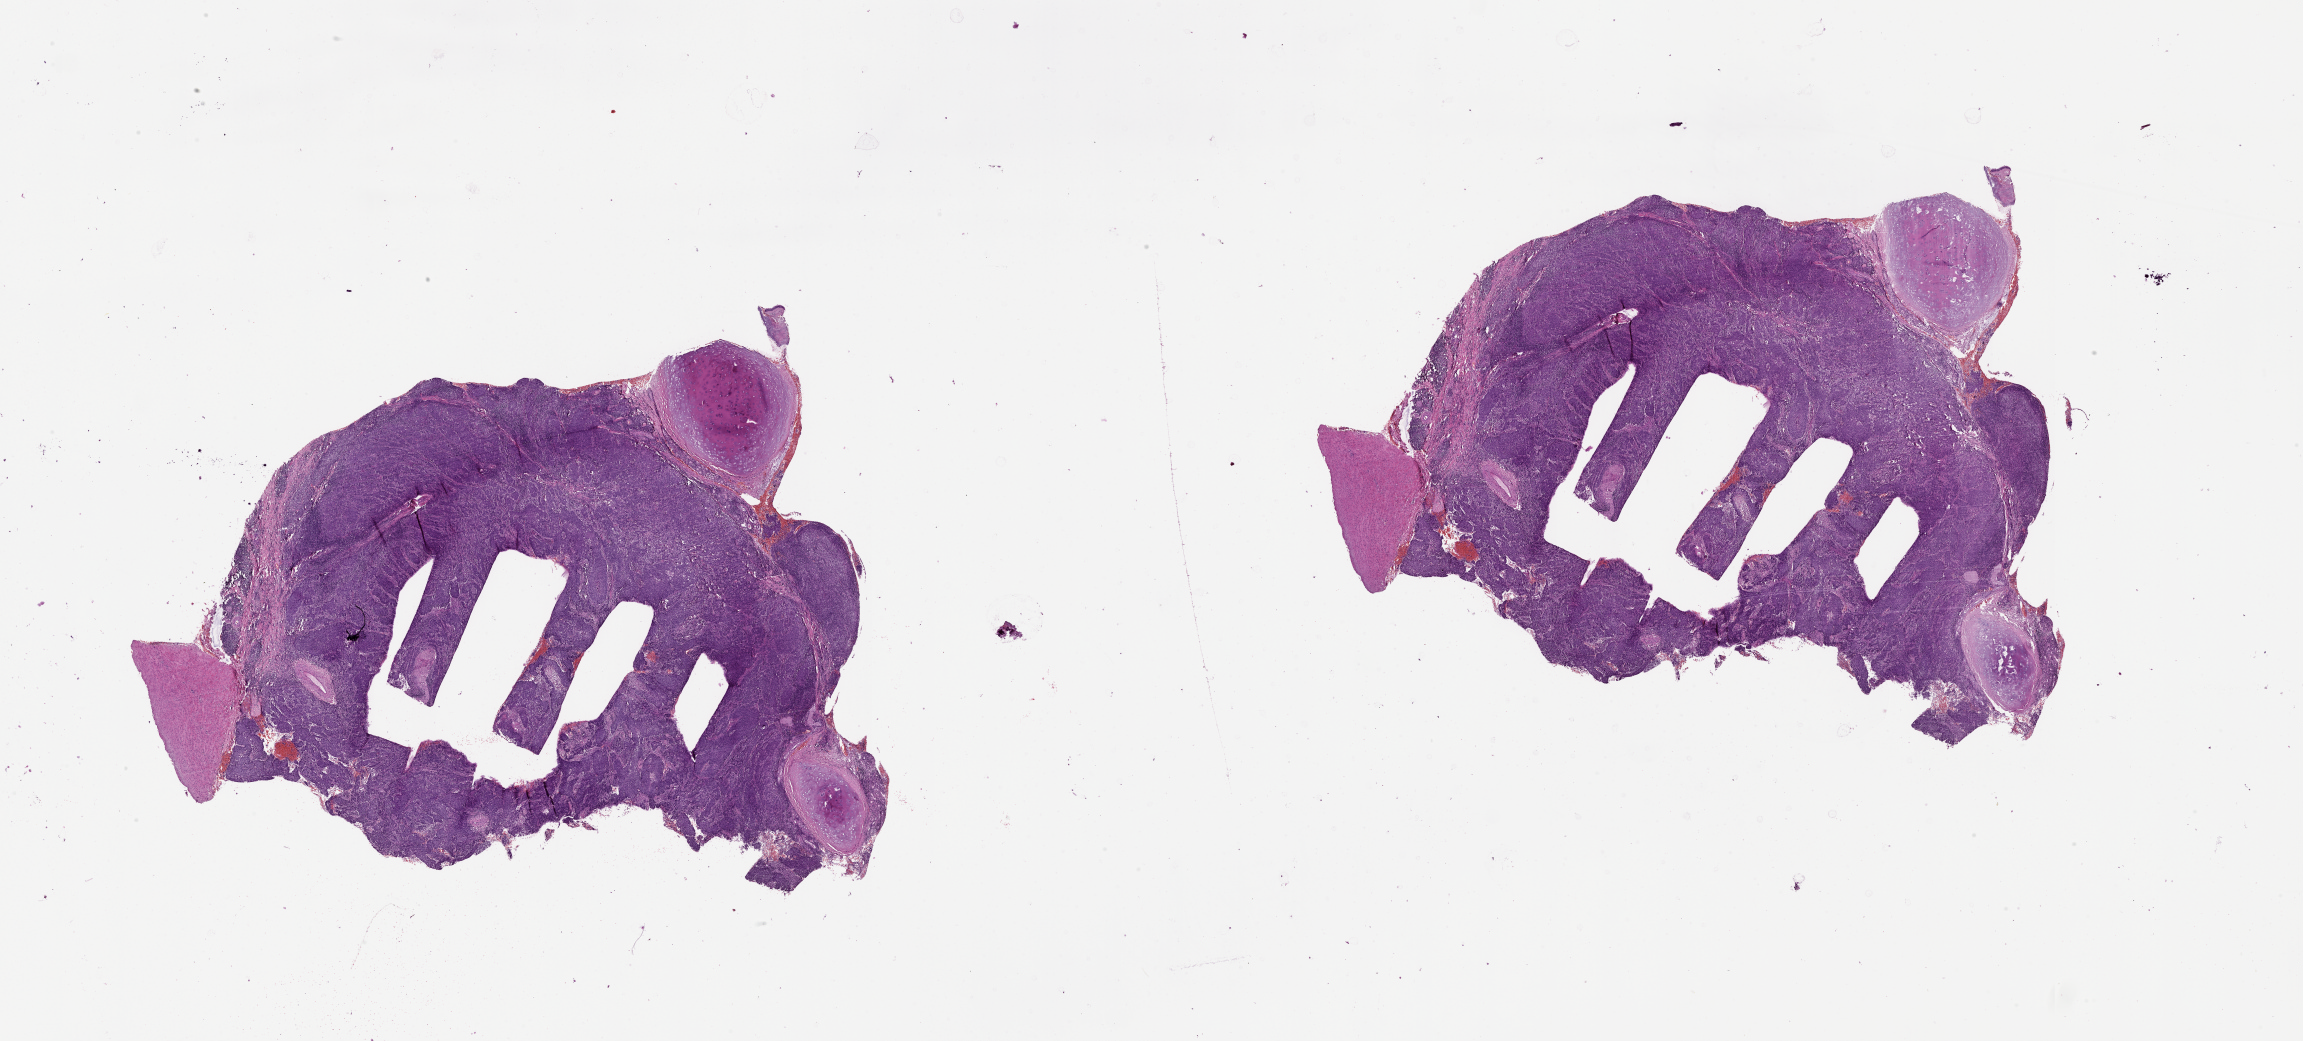
H&E-stained whole-slide image — a low-resolution overview of the entire scanned area, about 37.1 x 16.8 mm (slide scanned at 20x), lung, tumour tissue. 53-year-old male patient.
Patient diagnosis (cohort enrolment): squamous cell carcinoma (lung).